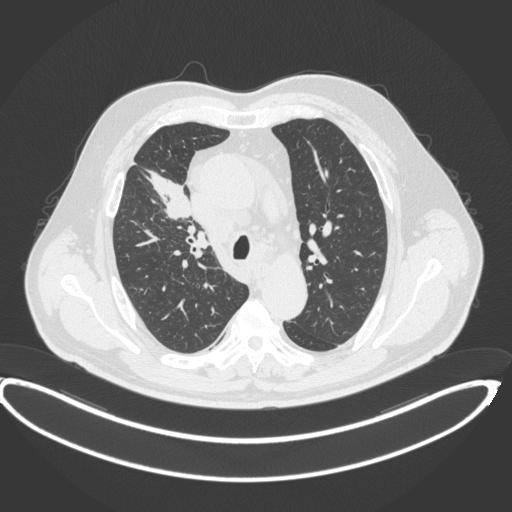
Chest CT, one axial slice. Slice 285 of 395 in the series (ordered by position). Reconstruction kernel B31f. 120 kVp. Lung window (W 1500 / L -600 HU). 1 mm slice thickness. 512 × 512 image matrix, field of view 448 × 448 mm. Patient: male, 62 years. From the clinical record (not read from this slice): clinical TNM (as recorded): T1c N3 M1c.
Outlined on this slice (rectangle marked by the reading radiologist):
- lung tumour (recorded histology: adenocarcinoma): box from (x=143, y=166) to (x=192, y=222) px